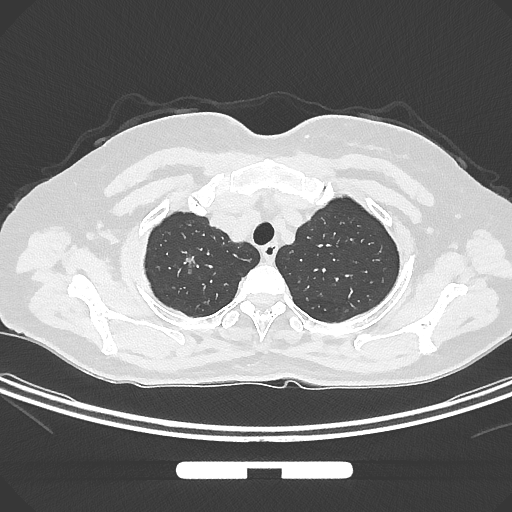
Chest CT, one axial slice. Slice 254 of 294 in the series (ordered by position). Lung window (W 1500 / L -600 HU). 1 mm slice thickness. 512 × 512 image matrix, field of view 369 × 369 mm. Patient: female, 58 years. From the clinical record (not read from this slice): clinical TNM (as recorded): T1b N0 M0; histopathological grade: G2-3.
Outlined on this slice (bounding box drawn by a radiologist):
- lung tumour (recorded histology: adenocarcinoma): bounding box [x1, y1, x2, y2] px = [177, 250, 200, 280]